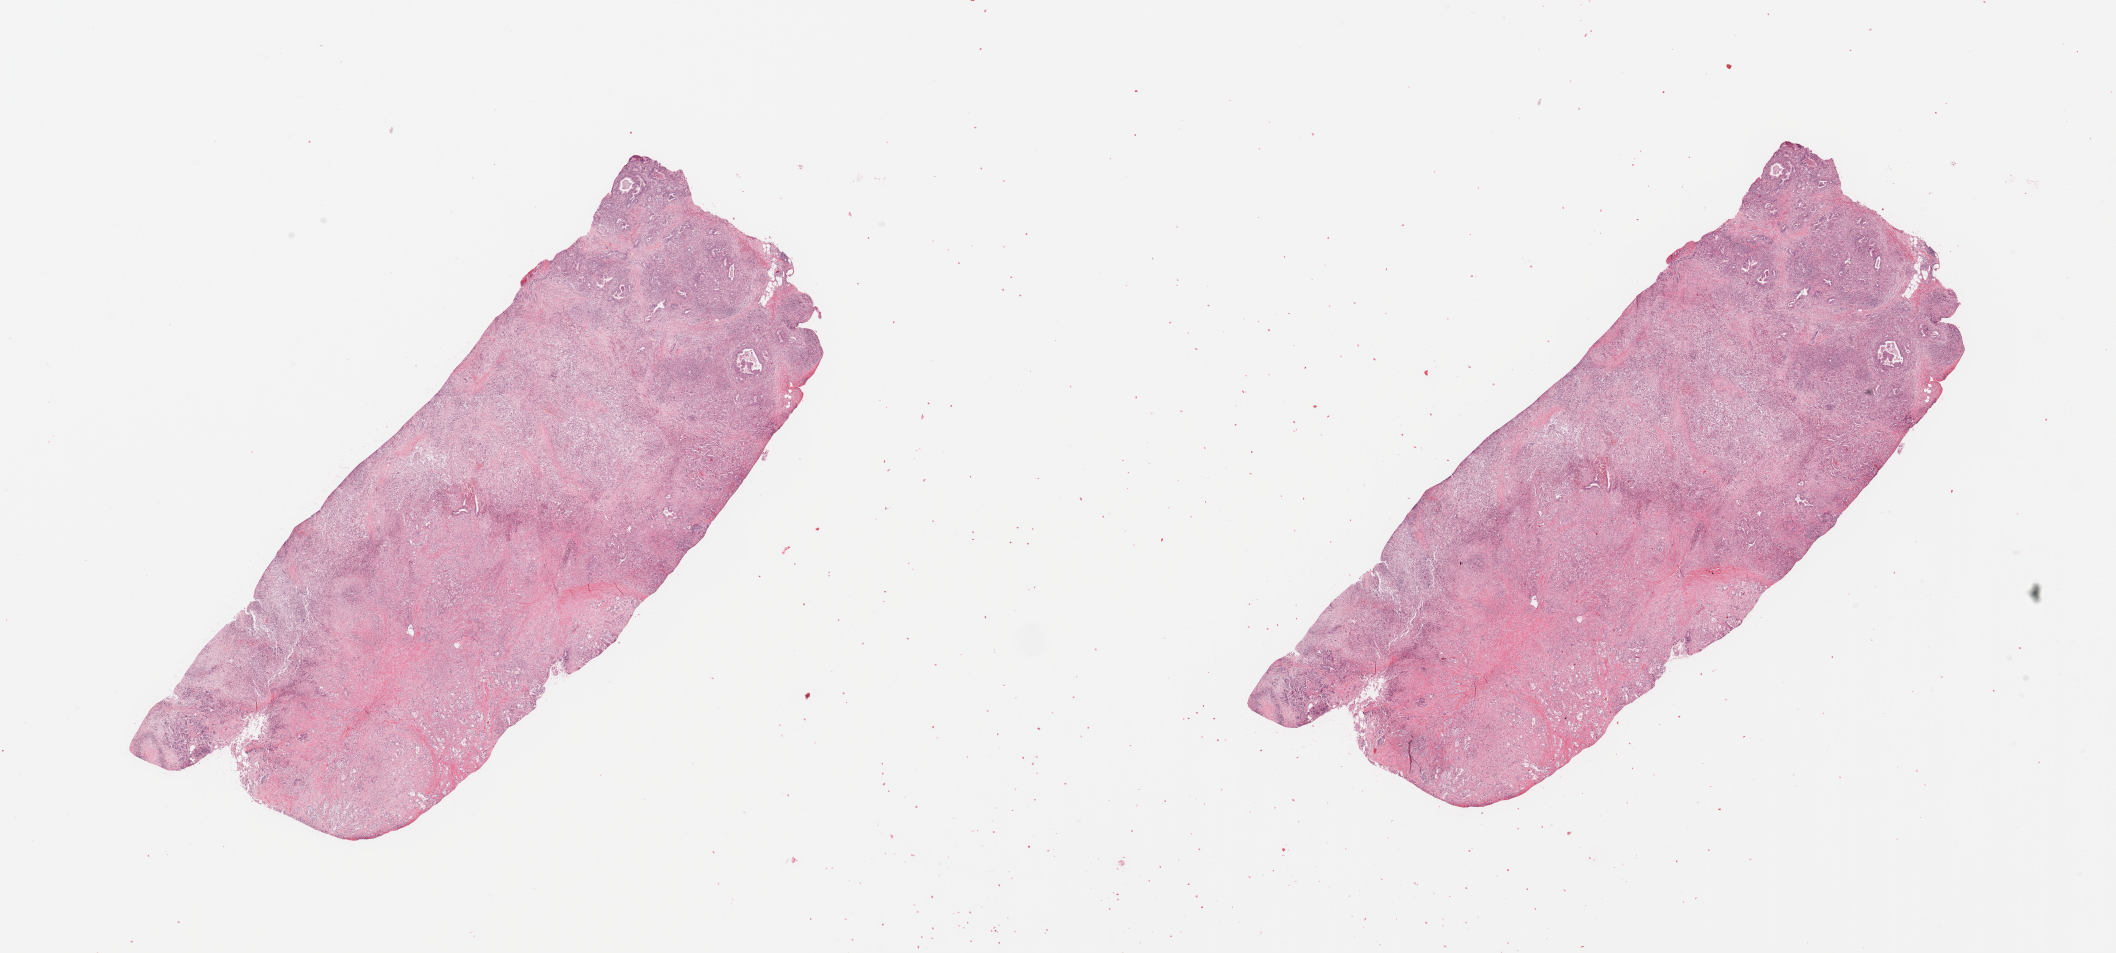
Whole-slide histology image, H&E — whole scanned area (about 33.5 x 15.1 mm, from a 20x scan) shown as a low-resolution overview, tumour tissue sample, pancreas. 84-year-old male patient.
Patient diagnosis (cohort enrolment): ductal adenocarcinoma (pancreas). Primary tumour site (as recorded): head.